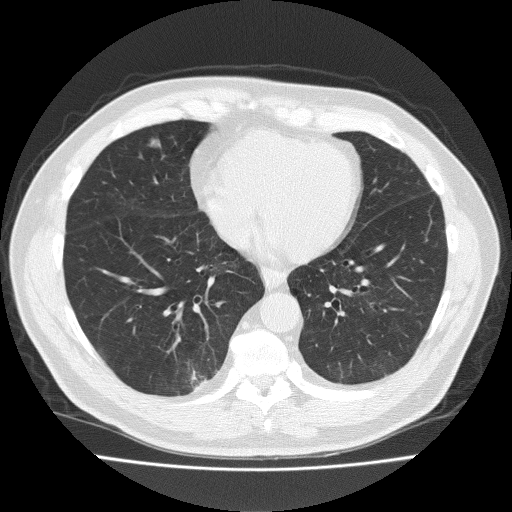
Chest CT (low-dose screening protocol), one axial image. Second annual screen. Lung window (W 1500 / L -600 HU). 2 mm slice thickness. Slice 119 of 184 in the series. Male, age 57 years at enrolment.
Expert-annotated lung lesion, bounding box (x1, y1, x2, y2) in pixels: (130, 131, 174, 168). Reader record for this screening exam (exam-level; its link to the box is not recorded): non-calcified nodule or mass ≥4 mm, right middle lobe, 8 × 7 mm, spiculated (stellate) margins, soft tissue attenuation, pre-existing on the prior screen: yes; interval growth: yes. Lung cancer was diagnosed 67 days after this screen: adenocarcinoma, NOS, right middle lobe, moderately differentiated (G2), stage IA (AJCC 6th edition), 12 mm at pathology.